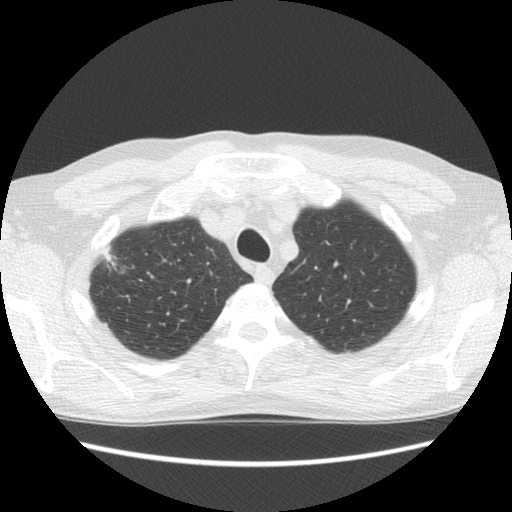
Low-dose screening chest CT, one axial slice; slice 103 of 125 in the series (ordered by position); reconstruction kernel STANDARD; 120 kVp; lung window (W 1500 / L -600 HU); 512 × 512 image matrix, field of view 350 × 350 mm.
Outlined on this slice (manually delineated by an expert):
- lesion 1 (tumor, upper lobe of right lung): bounding box (x1, y1, x2, y2) in pixels: (101, 249, 116, 265)